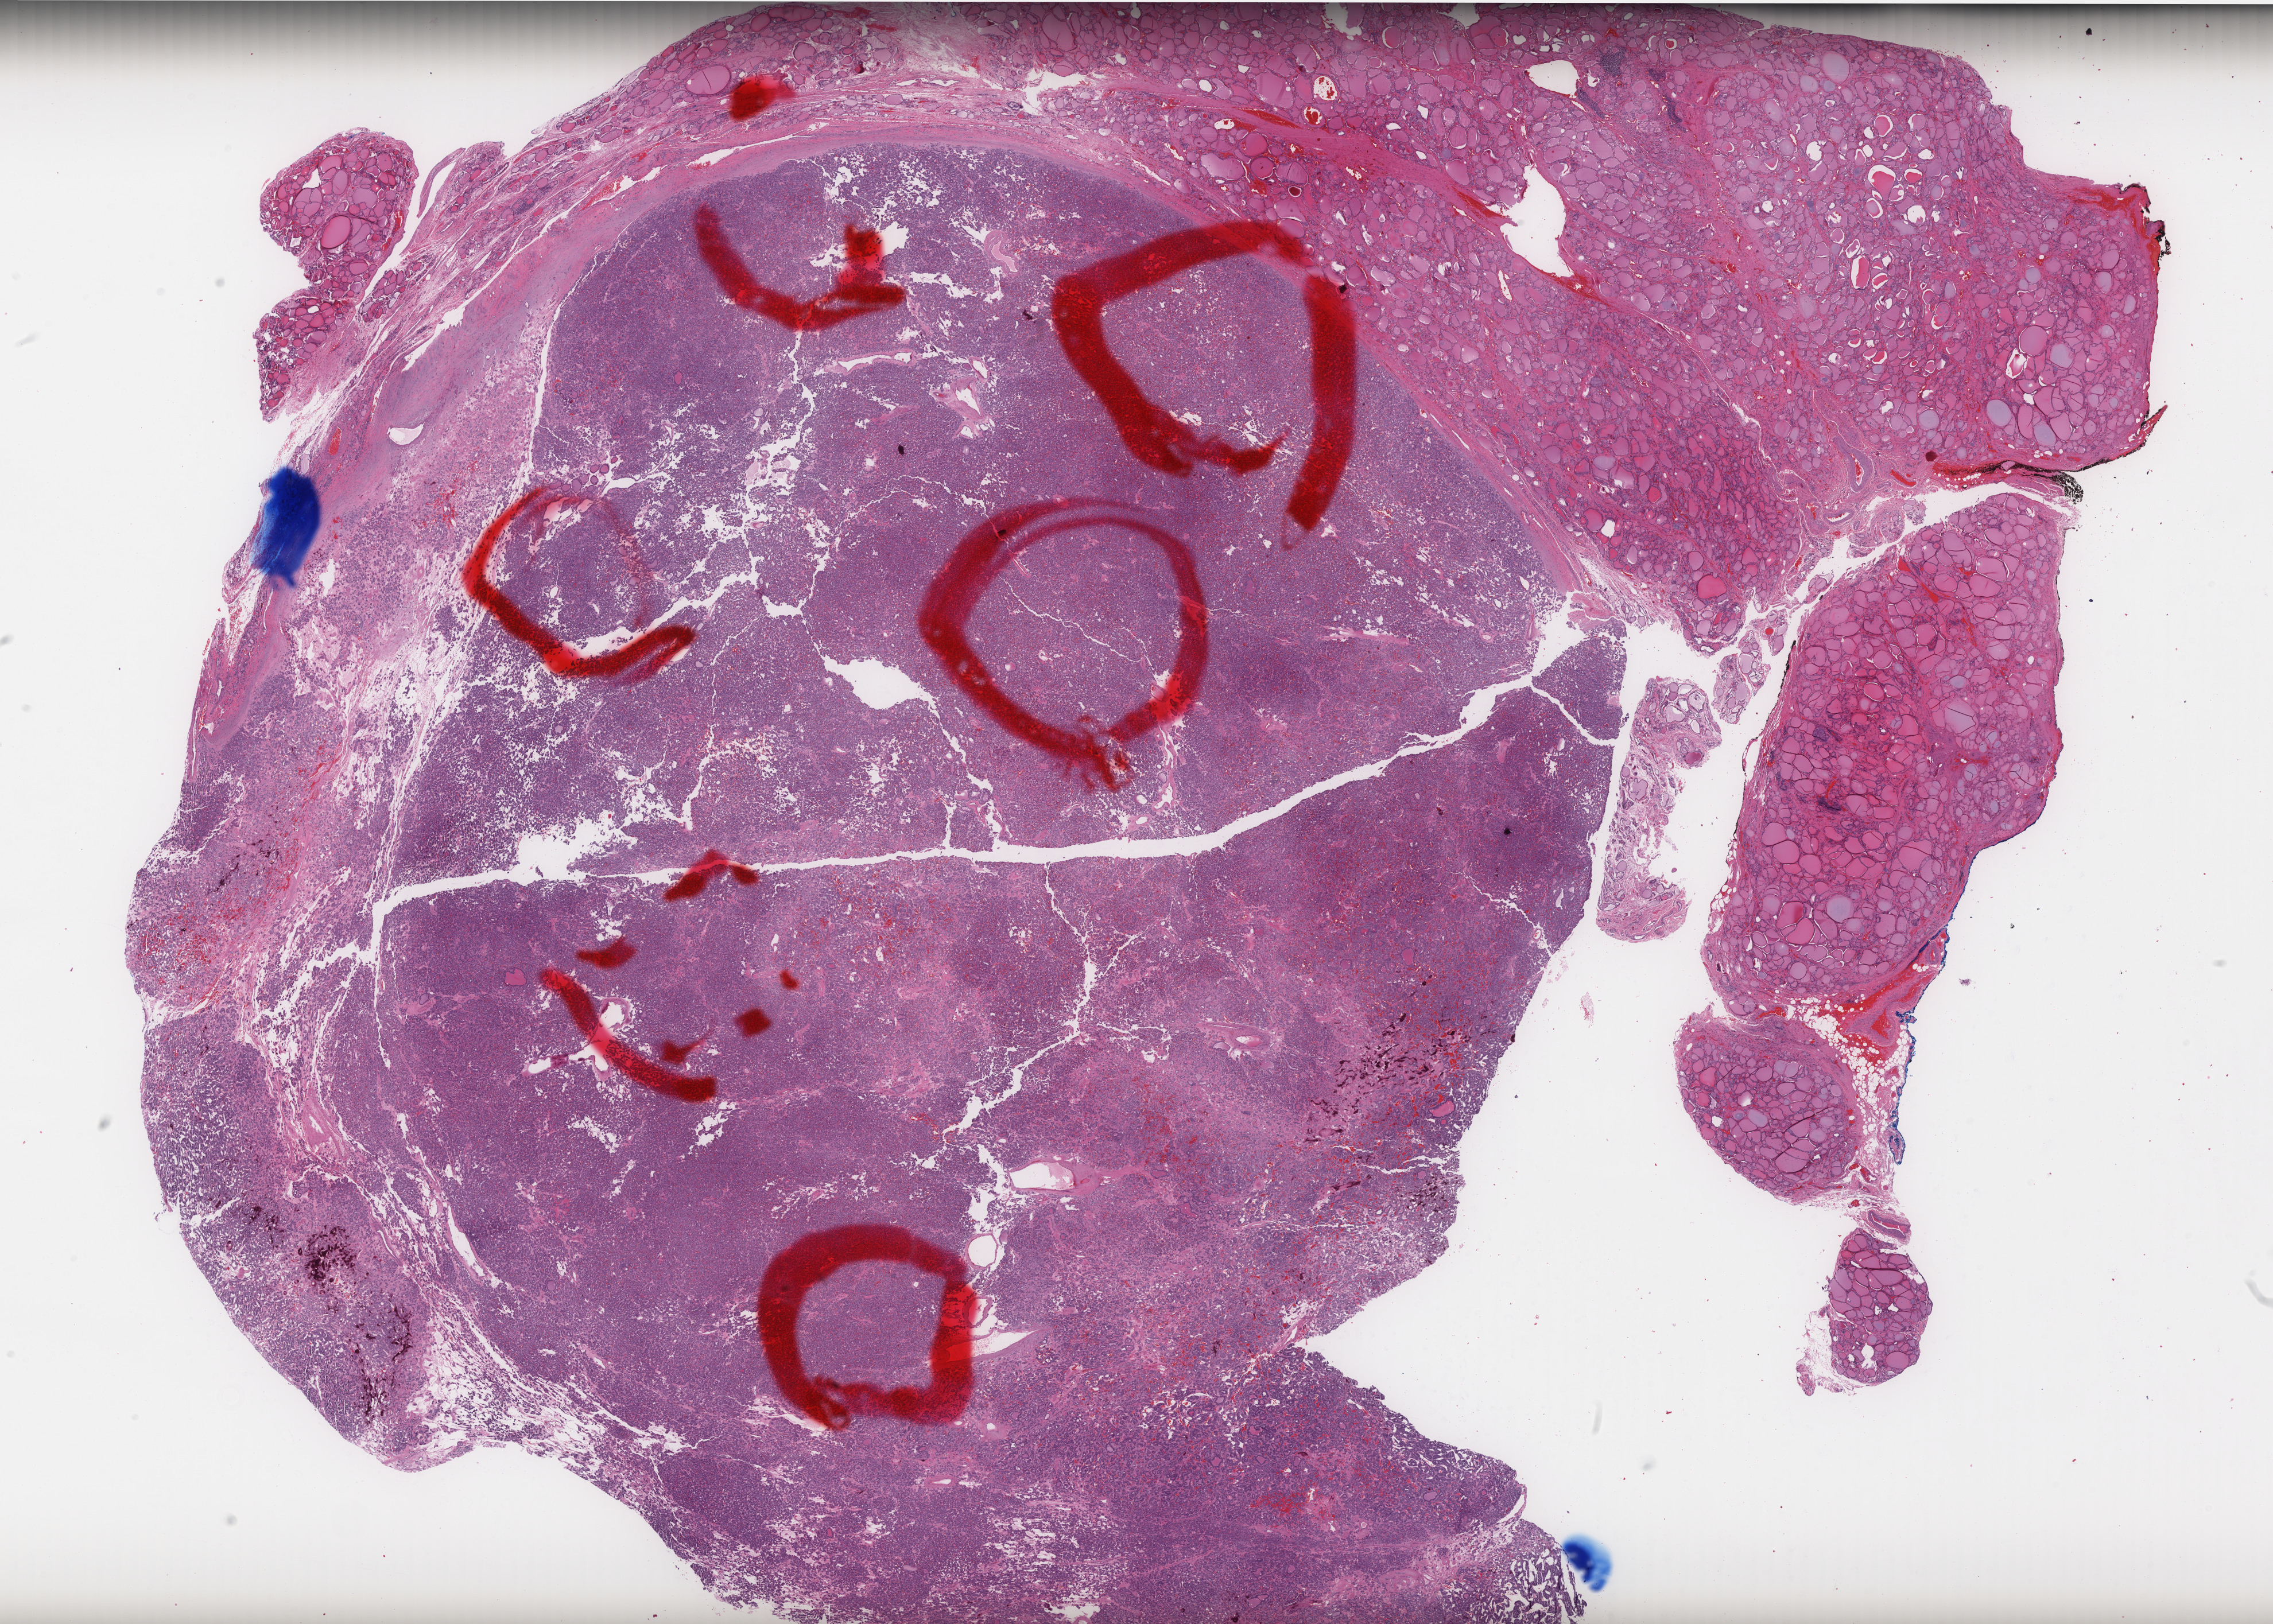
Digitized Hematoxylin and eosin (H&E) stained tissue section (whole slide), whole scanned area (about 31.7 x 22.7 mm, acquisition: 40x scan) shown as a low-resolution overview. Formalin-fixed paraffin-embedded (FFPE) diagnostic section. Primary tumour sample from the thyroid. Male patient; age at initial diagnosis 70 years.
TNM: T2 N0 M0. Histologic diagnosis: Papillary carcinoma, follicular variant. AJCC pathologic stage: II (7th edition).